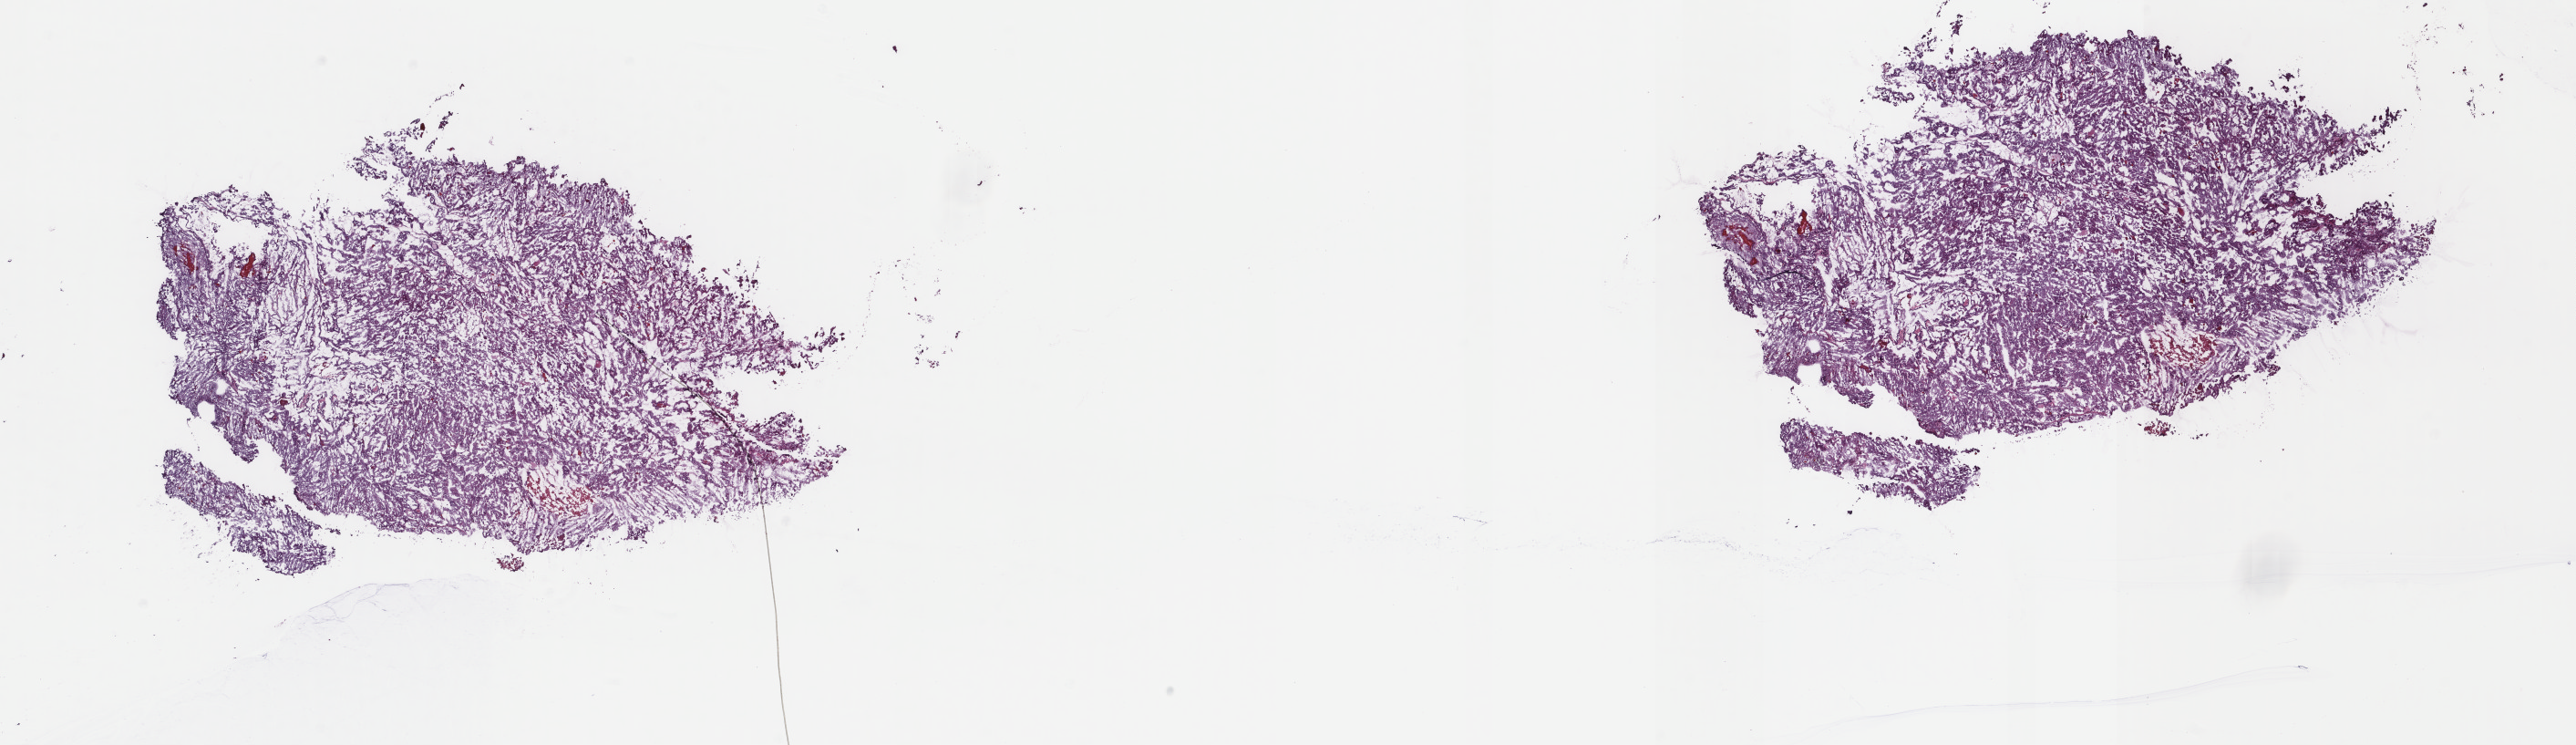
Whole-slide histology image, H&E-stained — a low-resolution overview of the entire scanned area, about 22.4 x 6.5 mm; frozen section; primary tumour sample from the thyroid. Male, age 40 years at initial diagnosis. Pathologist review of this section (percent, as recorded): tumour cells 100%, tumour nuclei 100%, normal cells 0%, stromal cells 0%, necrosis 0%. Inflammatory infiltration, as recorded: lymphocyte infiltration 0%, monocyte infiltration 0%, neutrophil infiltration 0%.
Laterality: right. TNM: T3 N0 MX. AJCC pathologic stage: I (7th edition). Pathologic diagnosis: Papillary carcinoma, follicular variant.